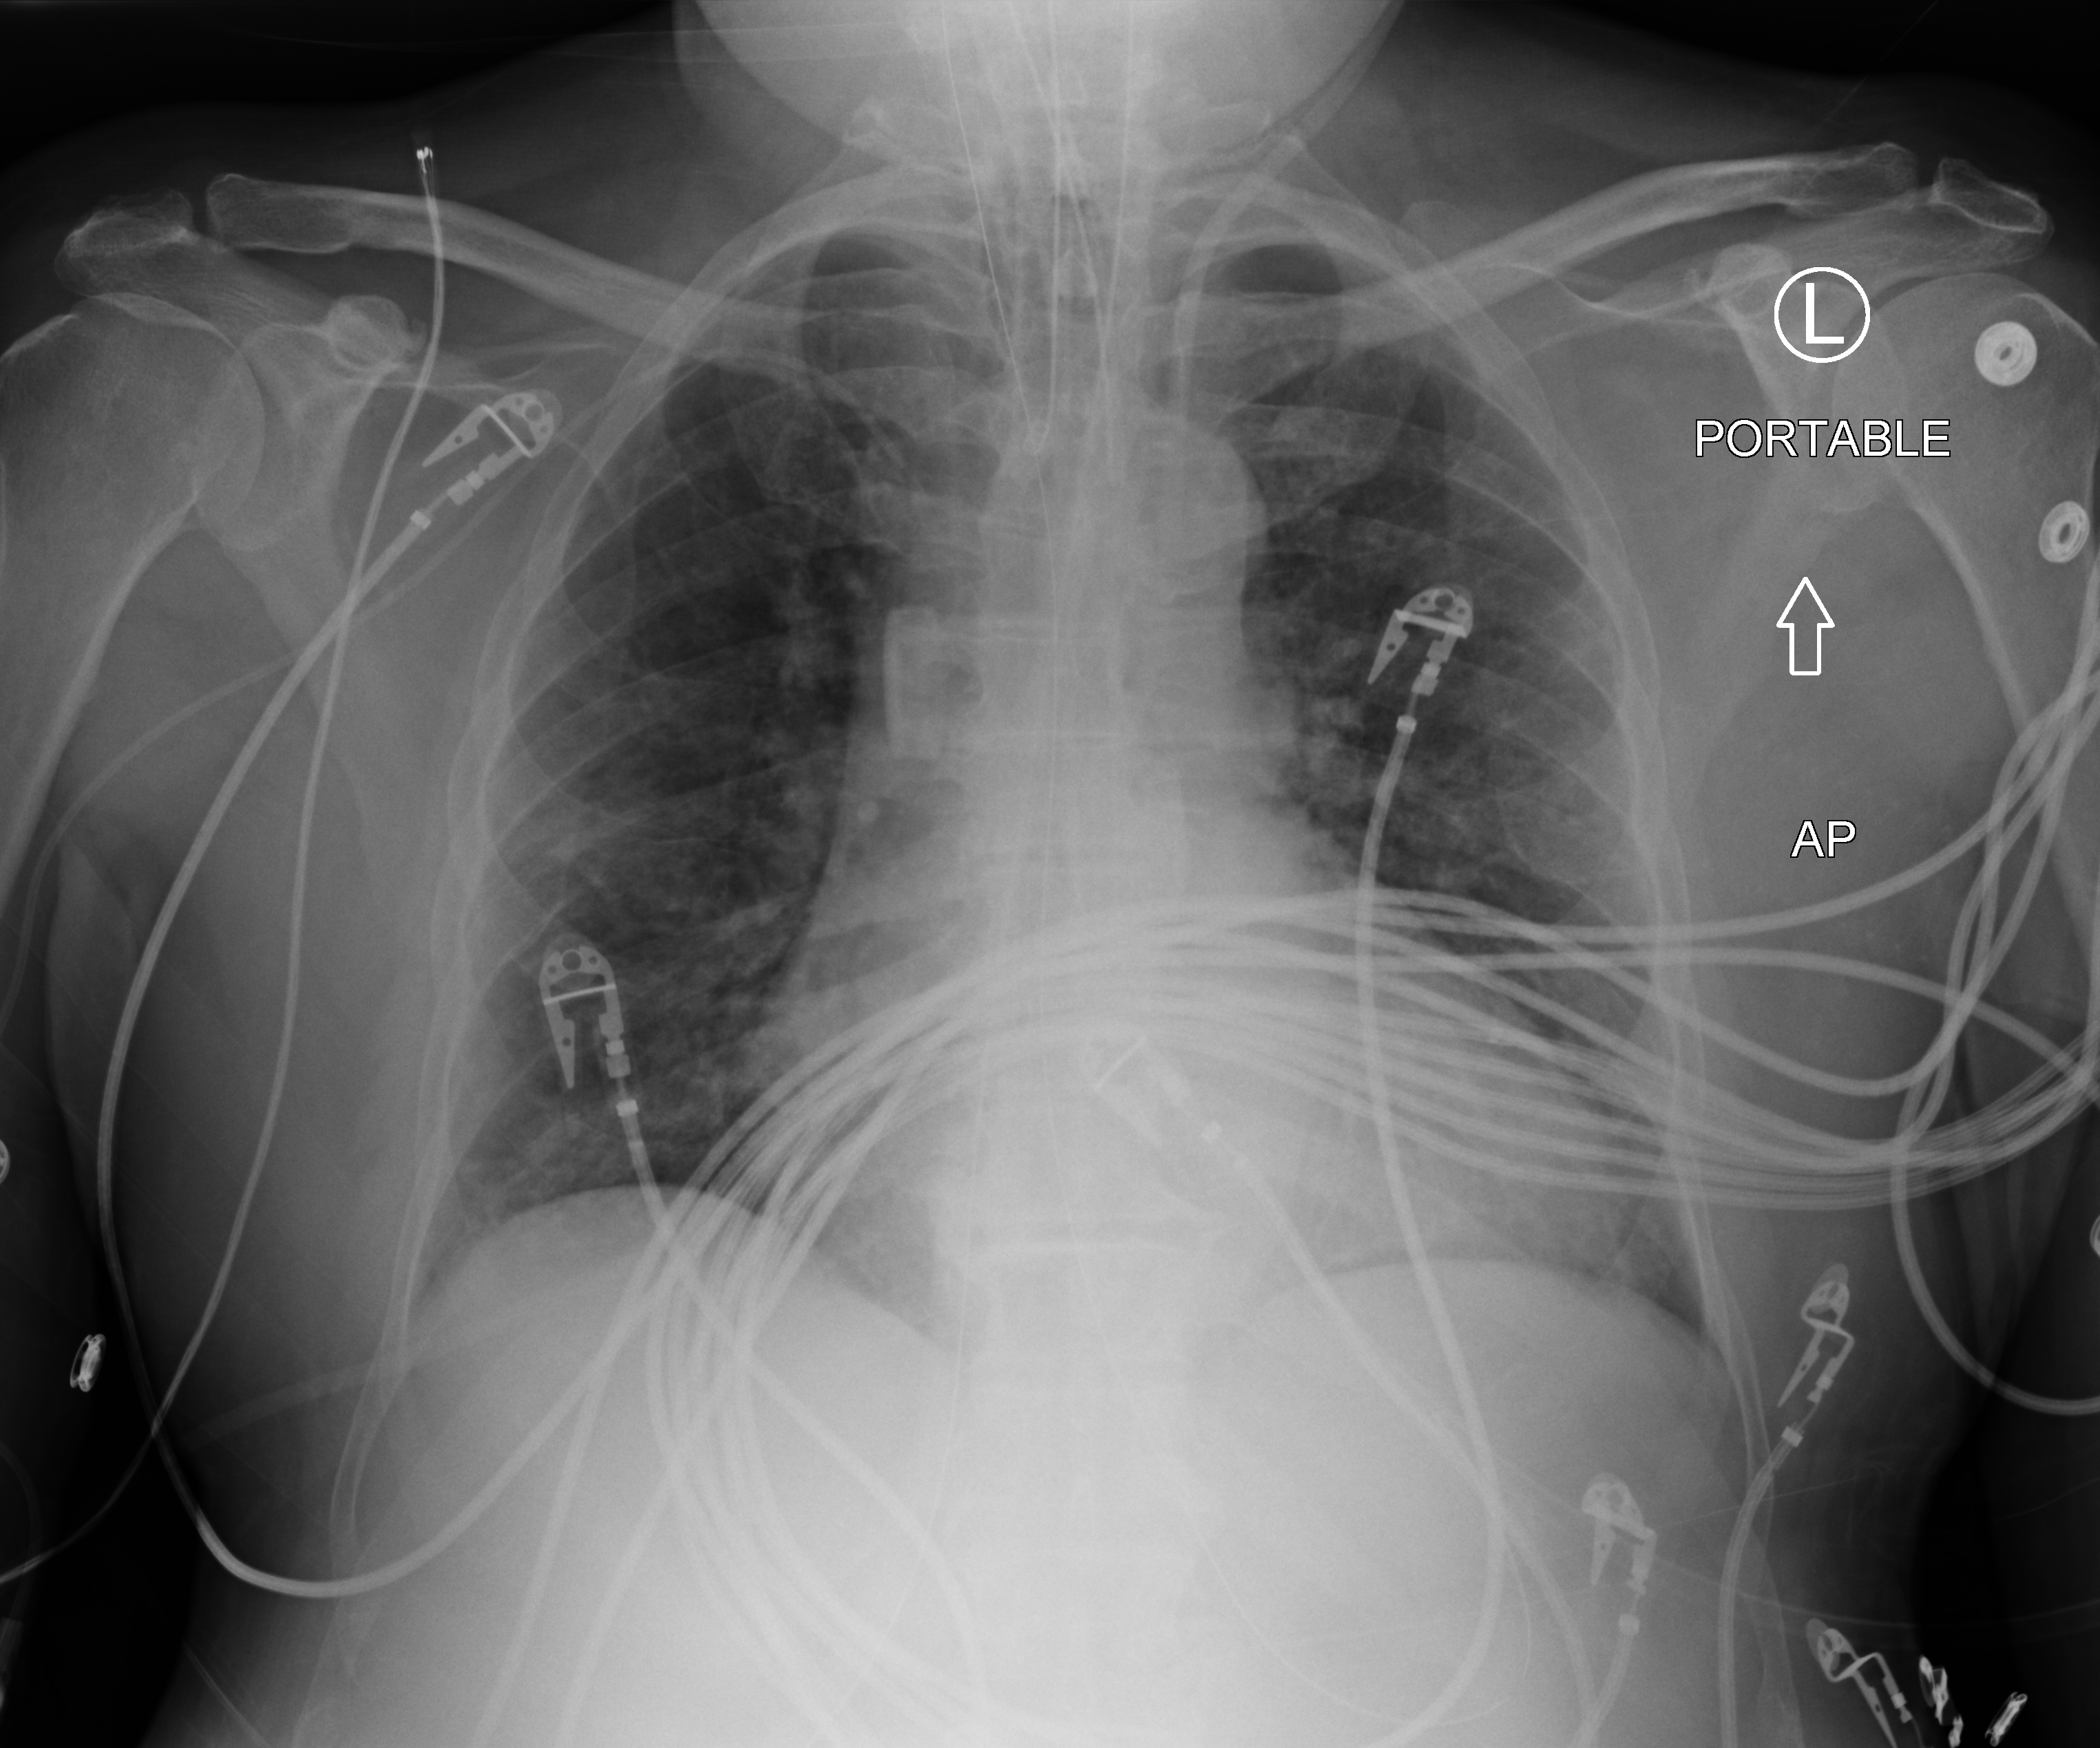
Bedside chest radiograph (computed radiography), anteroposterior (AP) projection. Patient hospitalised with COVID-19; male, aged 60–74 years.
Admission-level facts for this patient (not findings on this image; timing relative to this image not recorded):
- admitted to intensive care during this hospital stay: yes